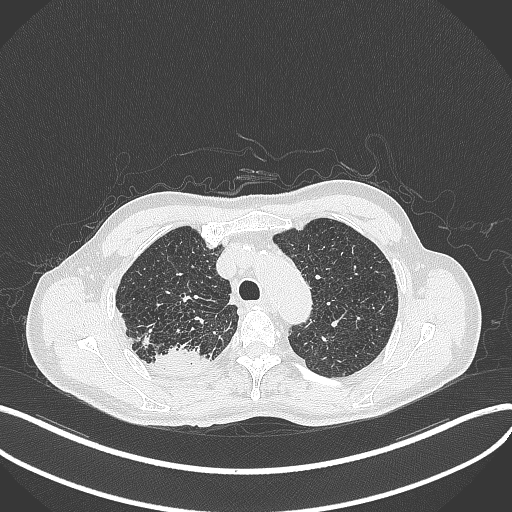
Chest CT, one axial slice; slice 345 of 428 in the series (ordered by position); reconstruction kernel B70f; lung window (W 1500 / L -600 HU); 512 × 512 image matrix, field of view 400 × 400 mm. Male patient, age 79 years. Case-level facts recorded for this patient, not image findings: clinical TNM (as recorded): T3 N0 M0.
Annotated regions visible in this slice (rectangle marked by the reading radiologist):
- lung tumour (recorded histology: adenocarcinoma): bounding box [x1, y1, x2, y2] px = [149, 341, 201, 371]